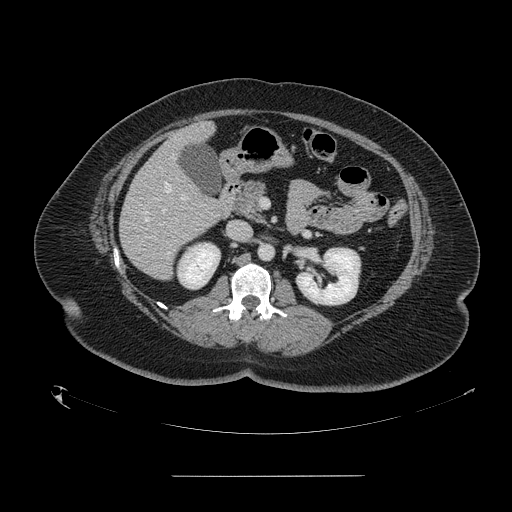
Contrast-enhanced abdominal CT, one axial slice. Position 70 of 164 along the scan axis. 120 kVp. Intravenous contrast given. Soft-tissue window (W 400 / L 40 HU). 2.5 mm slice thickness. 512 × 512 image matrix. Female patient, age 52 years. Case-level facts recorded for this patient, not image findings: diagnosis: colorectal cancer liver metastases, imaged before liver resection; multiple liver metastases: yes; largest metastasis: 3.5 cm.
Outlined on this slice (manually delineated by an expert):
- hepatic veins: bounding box <144,183,171,221> (left, top, right, bottom; pixels)
- liver: <120,123,231,279>
- planned liver remnant (the part of the liver to remain after resection): <180,123,214,146>
- portal vein (with intrahepatic branches): <181,197,185,200>